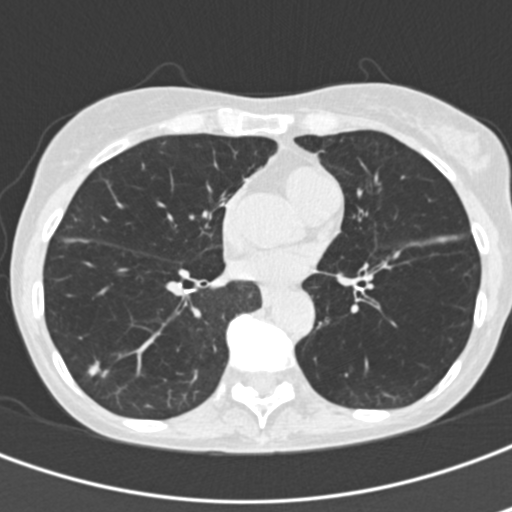
Chest CT (low-dose screening protocol), one axial image, second screening round (one year after baseline), lung window (W 1500 / L -600 HU), 2 mm slice thickness, standard (soft-tissue) reconstruction kernel (B30f), slice 102 of 201 in the series, 512 × 512 image matrix, field of view 280 × 280 mm. Female, age 68 years at enrolment. Former smoker at enrolment.
Lesion marked by an expert reader, bounding box [x1, y1, x2, y2] px = [76, 352, 116, 391]. Screening reader's record for this exam (one nodule recorded; not confirmed to be the boxed lesion): non-calcified nodule or mass ≥4 mm, right lower lobe, 9 × 7 mm, spiculated (stellate) margins, soft tissue attenuation, pre-existing on the prior screen: yes; interval growth: yes. Official screen result: positive, other. Later outcome: lung cancer diagnosed 659 days after this screen (after the third annual screen) — squamous cell carcinoma, NOS, right lower lobe, stage IA (AJCC 6th edition).